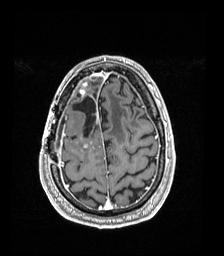
Brain MRI from a brain-tumour surgery series, one axial slice; slice 43 of 192 in the series (ordered by position); T1-weighted post-contrast; 1 mm slice thickness; 224 × 256 image matrix, field of view 224 × 256 mm. Case-level facts recorded for this patient, not image findings: histopathology: Astrocytoma; WHO grade: 4; IDH mutation: yes; tumour location: Right Frontal.
Annotated regions visible in this slice (outlined manually by an expert reader):
- previous resection cavity: bounding box [x1, y1, x2, y2] px = [73, 96, 96, 137]
- tumour: [79, 82, 89, 97]